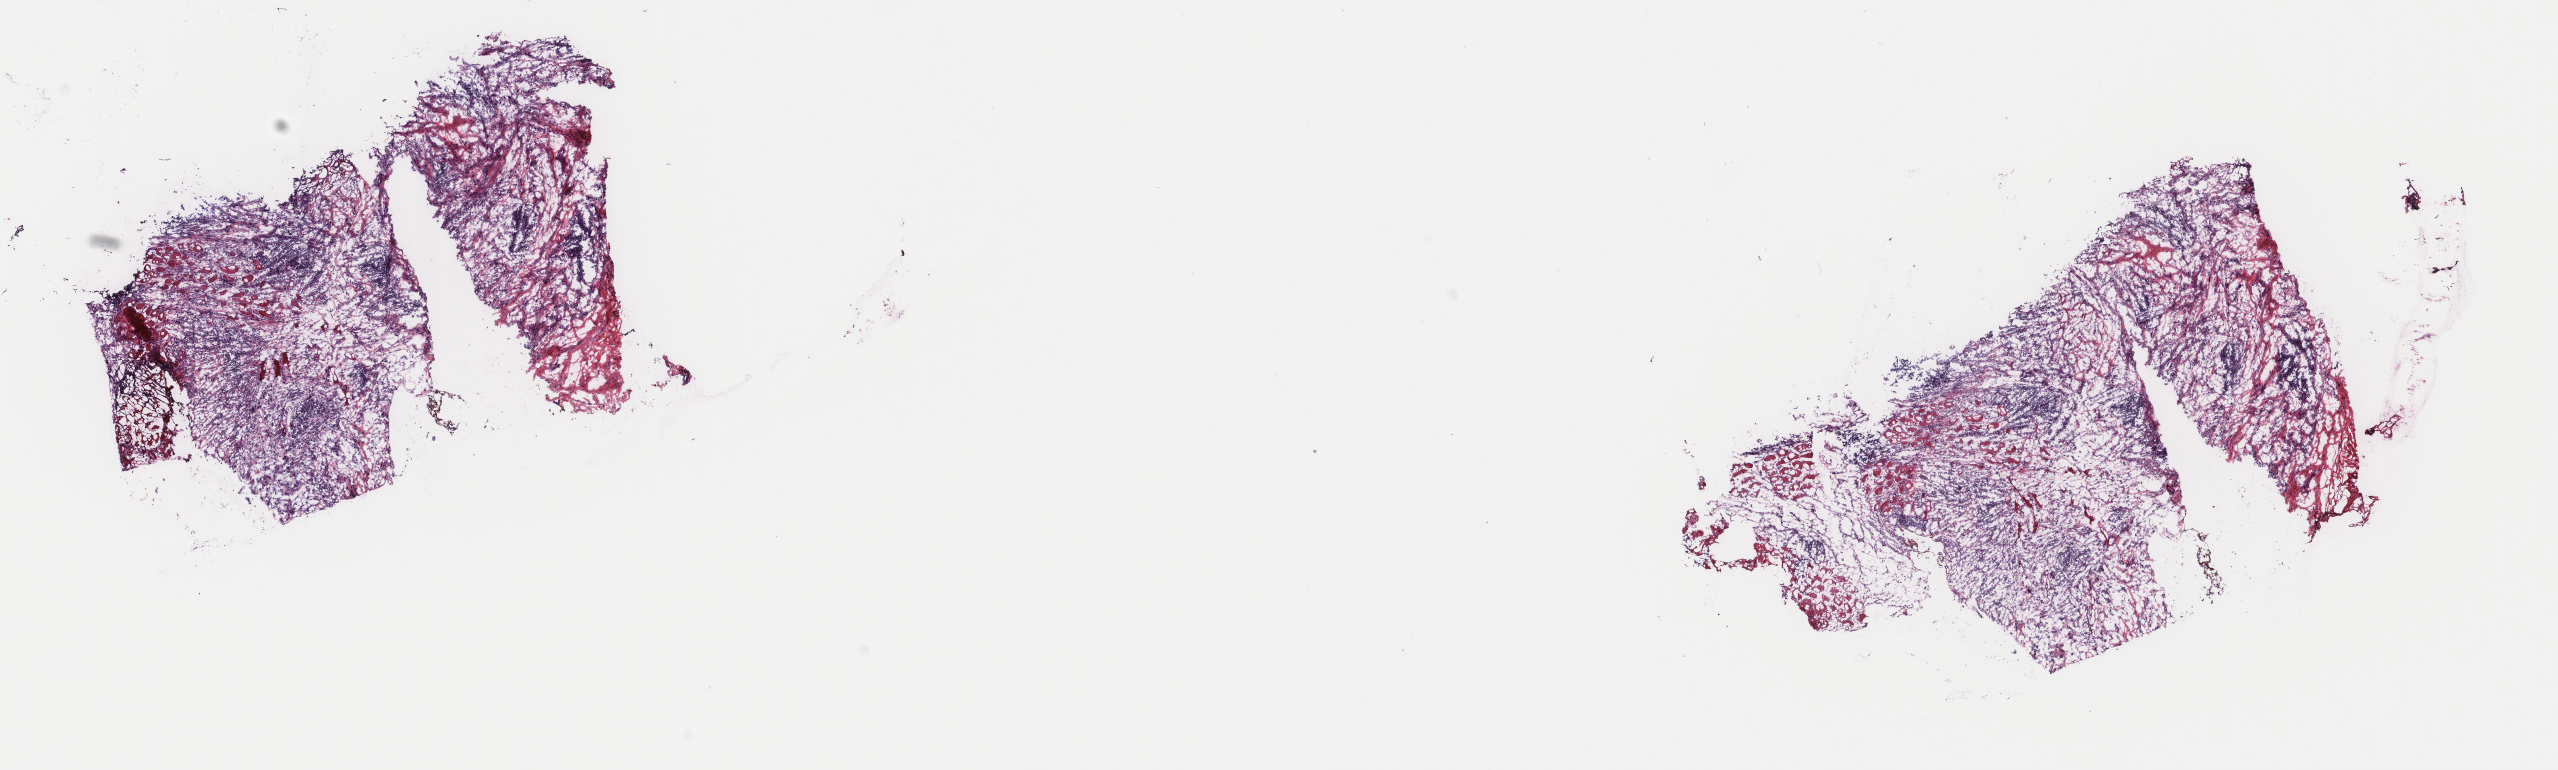
H&E-stained whole-slide image, shown as a low-resolution overview of the whole scanned area (about 20.3 x 6.1 mm, slide scanned at 40x), frozen section, primary tumour sample from the connective, subcutaneous and other soft tissues. Male patient; age at initial diagnosis 48 years. Pathologist review of this section (percent, as recorded): tumour cells 100%, tumour nuclei 70%, normal cells 0%, stromal cells 0%, necrosis 0%. Infiltration values recorded for this section: lymphocyte infiltration 3%, monocyte infiltration 0%, neutrophil infiltration 0%.
* pathologic diagnosis: Leiomyosarcoma, NOS (connective, subcutaneous and other soft tissues of lower limb and hip)